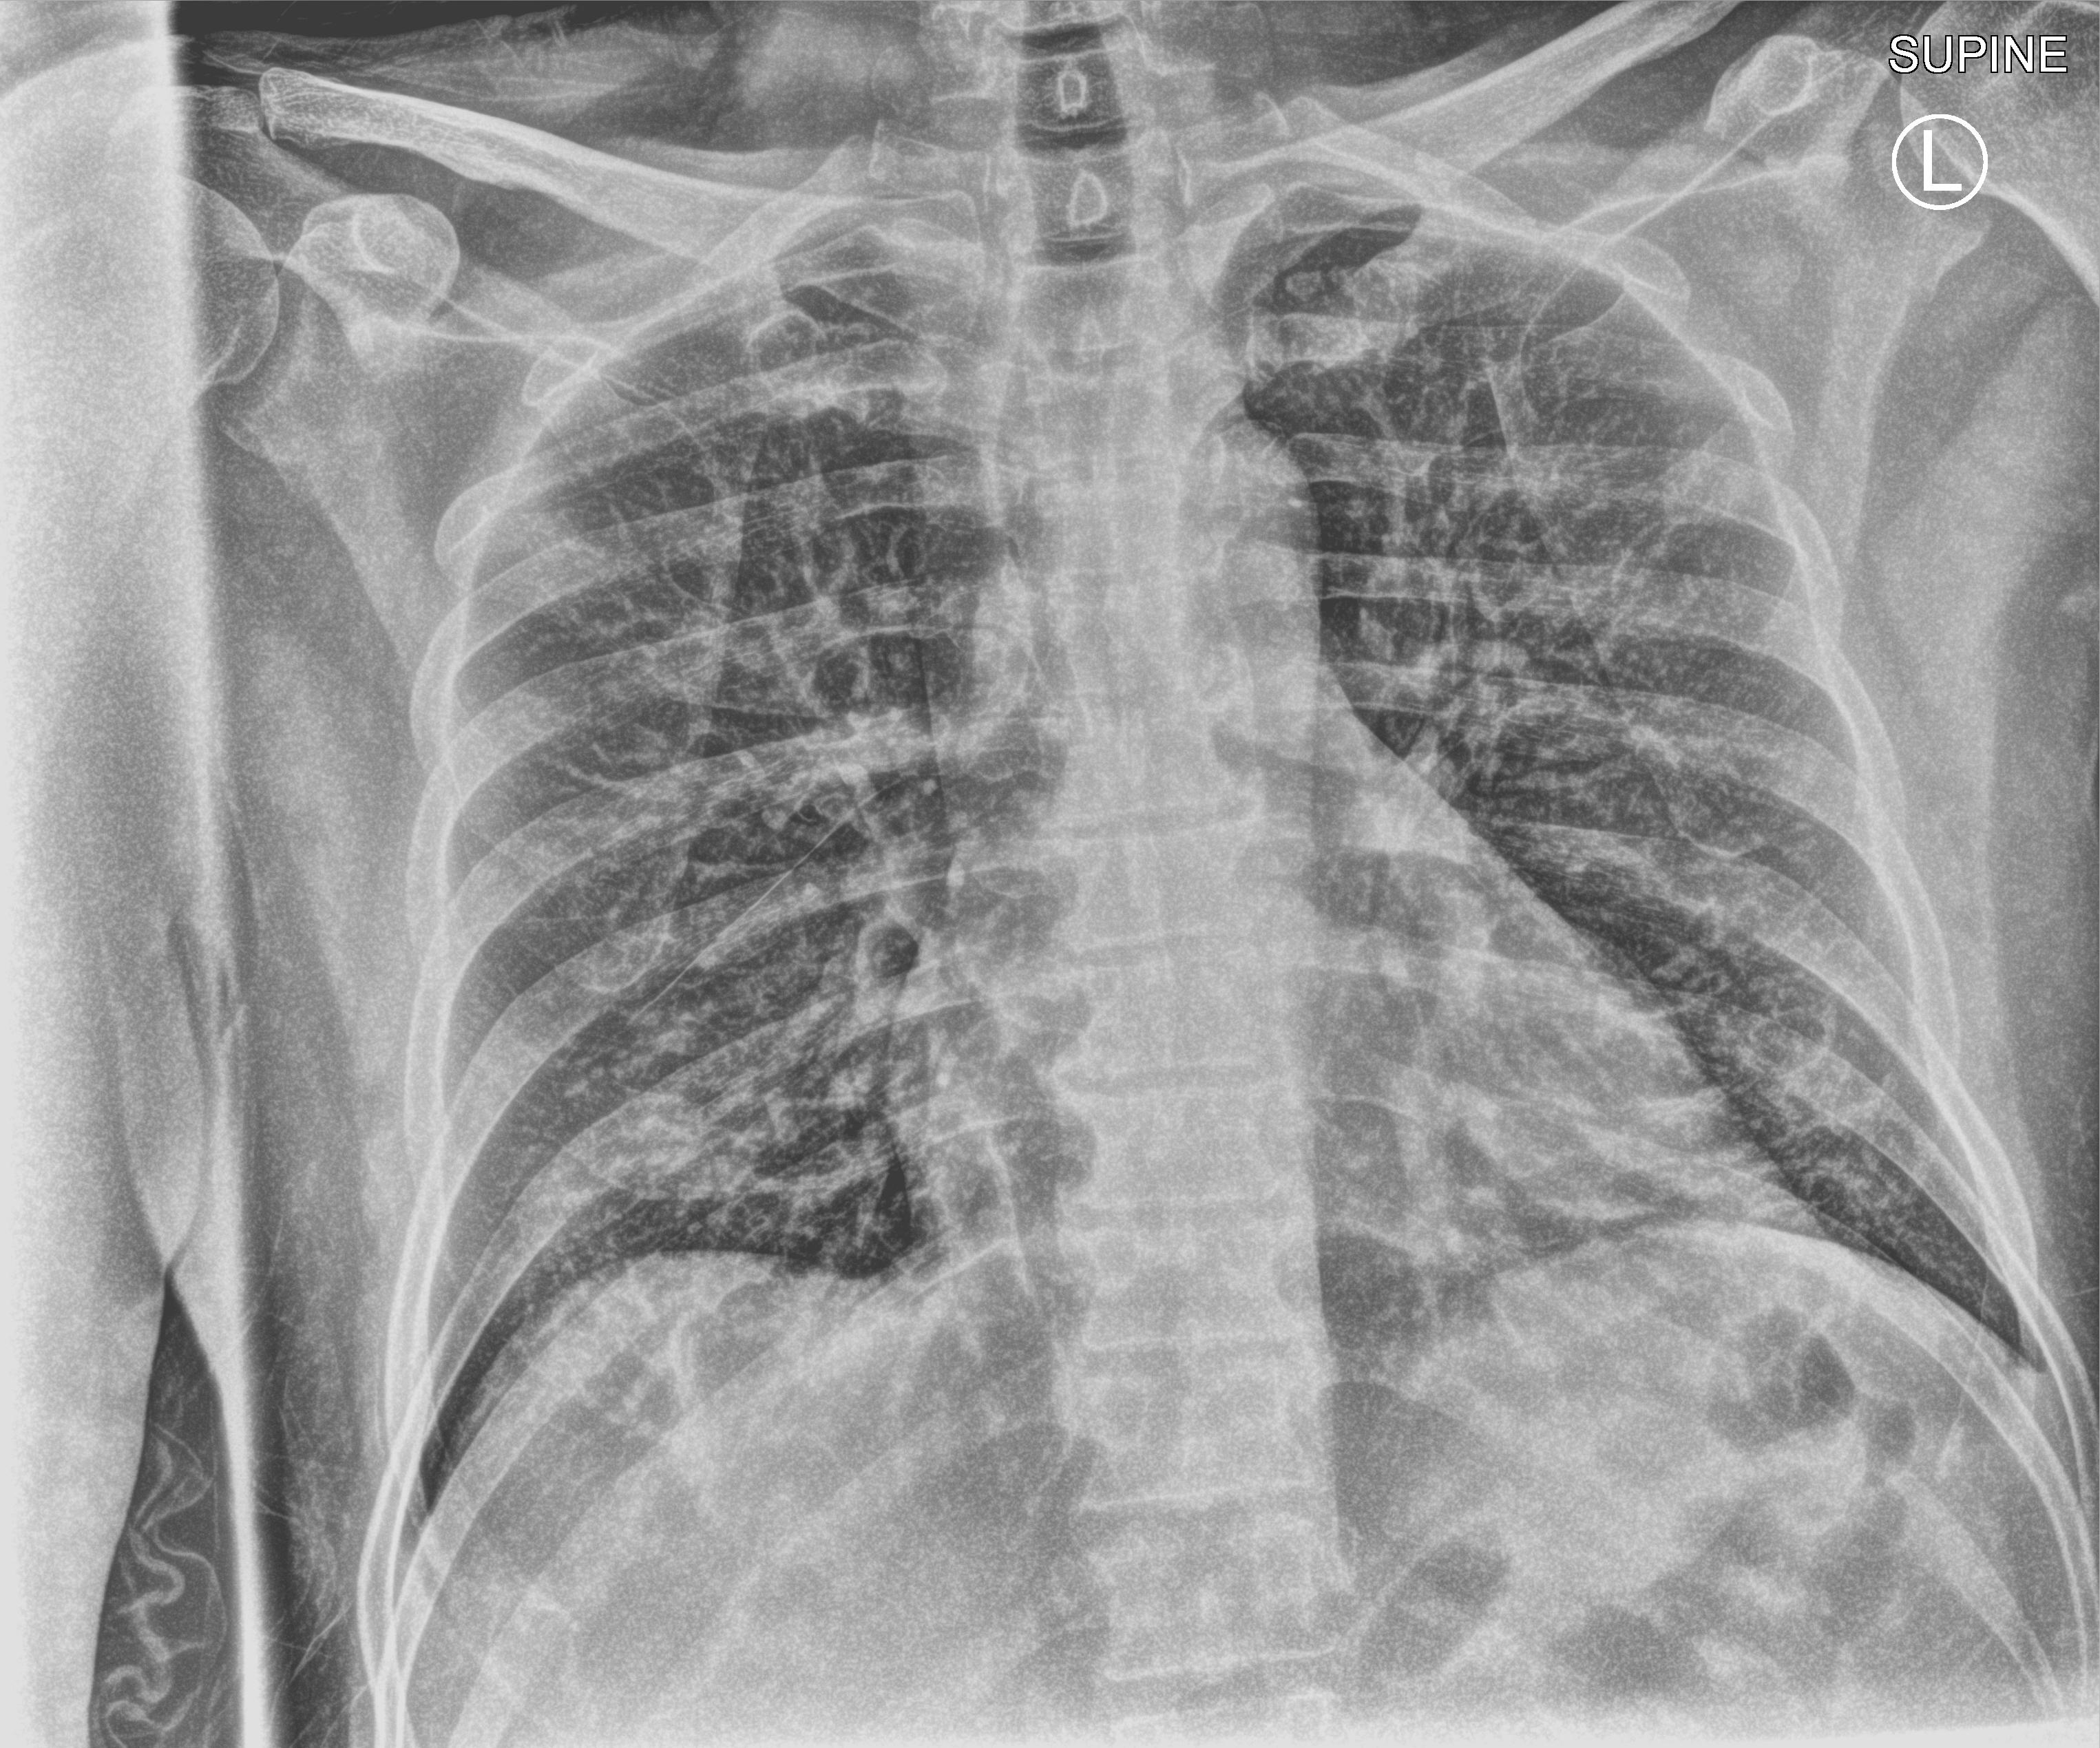
Chest X-ray (portable). Patient hospitalised with COVID-19; male, aged 18–59 years.
Hospital-stay facts (about this admission, not read from this image; timing relative to this image not recorded):
- mechanically ventilated during this hospital stay: no
- admitted to intensive care during this hospital stay: no